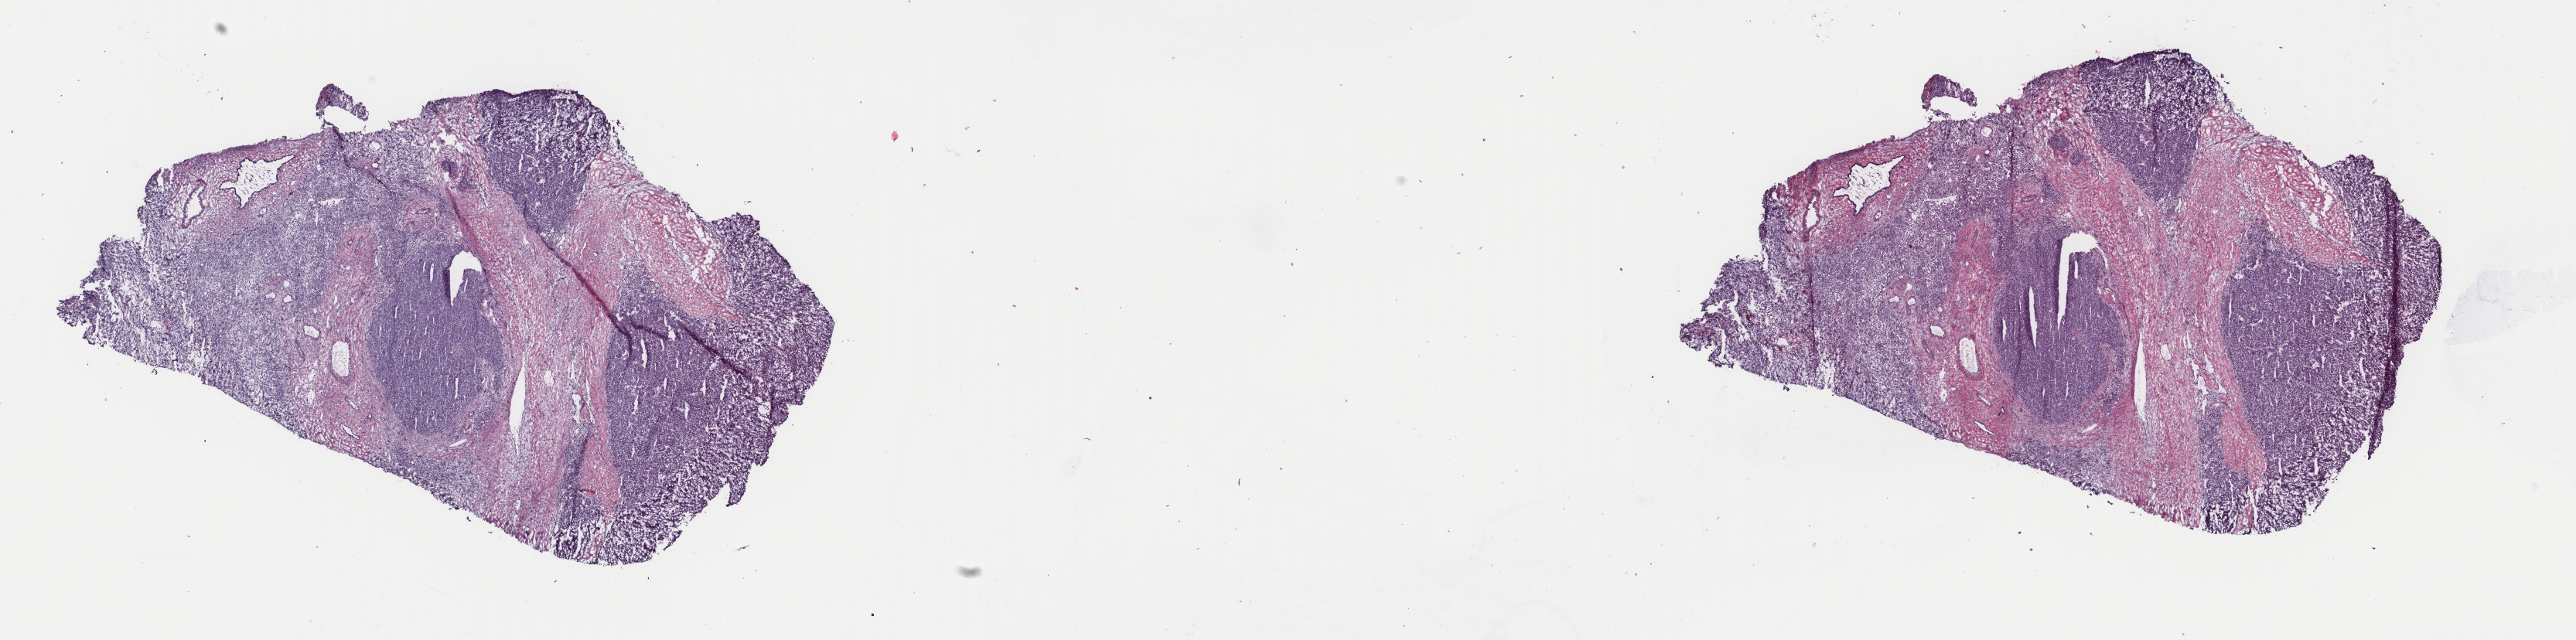
Hematoxylin and eosin (H&E) stained whole-slide image, shown as a low-resolution overview of the whole scanned area (about 26.4 x 6.6 mm), frozen section from the top of the tissue portion, sample: primary tumour, liver. Female patient; age at initial diagnosis 56 years. Histologic grade: G3 (poorly differentiated). Slide review estimates, as recorded: tumour cells 100%, tumour nuclei 75%, normal cells 0%, stromal cells 0%, necrosis 0%. Infiltration values recorded for this section: lymphocyte infiltration 3%, monocyte infiltration 0%, neutrophil infiltration 0%.
AJCC pathologic stage: I. Histologic diagnosis: Hepatocellular carcinoma, NOS. TNM: T1 N0 M0.